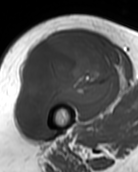
MRI of an extremity soft-tissue mass, one axial slice; slice 62 of 99 in the series (ordered by position); MR volume resampled by the dataset authors to the PET/CT grid (not the native acquisition matrix); 3.27 mm slice thickness; 138 × 172 image matrix, field of view 135 × 168 mm. Female patient. Case-level facts recorded for this patient, not image findings: histological type: pleiomorphic undifferentiated sarcoma; grade: high; site of the primary tumour: right quadricep.
Annotated regions visible in this slice (expert contour drawn on MRI and transferred to this co-registered scan by the dataset authors):
- gross tumour volume including surrounding oedema: bounding box <16,36,116,131> (left, top, right, bottom; pixels)
- gross tumour volume (mass): <16,36,116,131>